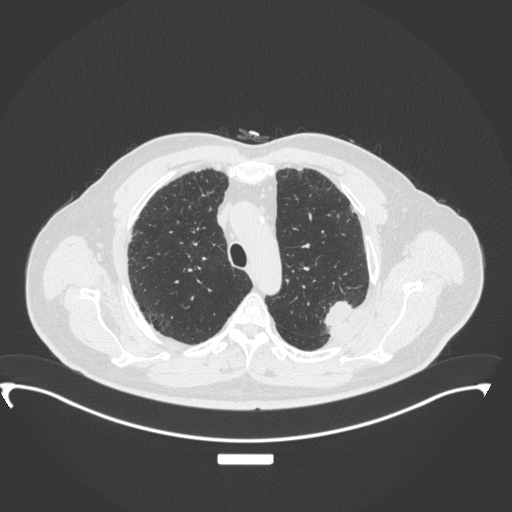
Chest CT, one axial slice; position 275 of 350 along the scan axis; lung window (W 1500 / L -600 HU); 1 mm slice thickness; 512 × 512 image matrix, field of view 459 × 459 mm. Male patient, age 64 years. From the clinical record (not read from this slice): clinical TNM (as recorded): T1c N1 M1.
Annotated regions visible in this slice (bounding box drawn by a radiologist):
- lung tumour (recorded histology: adenocarcinoma): bounding box <320,295,358,337> (left, top, right, bottom; pixels)